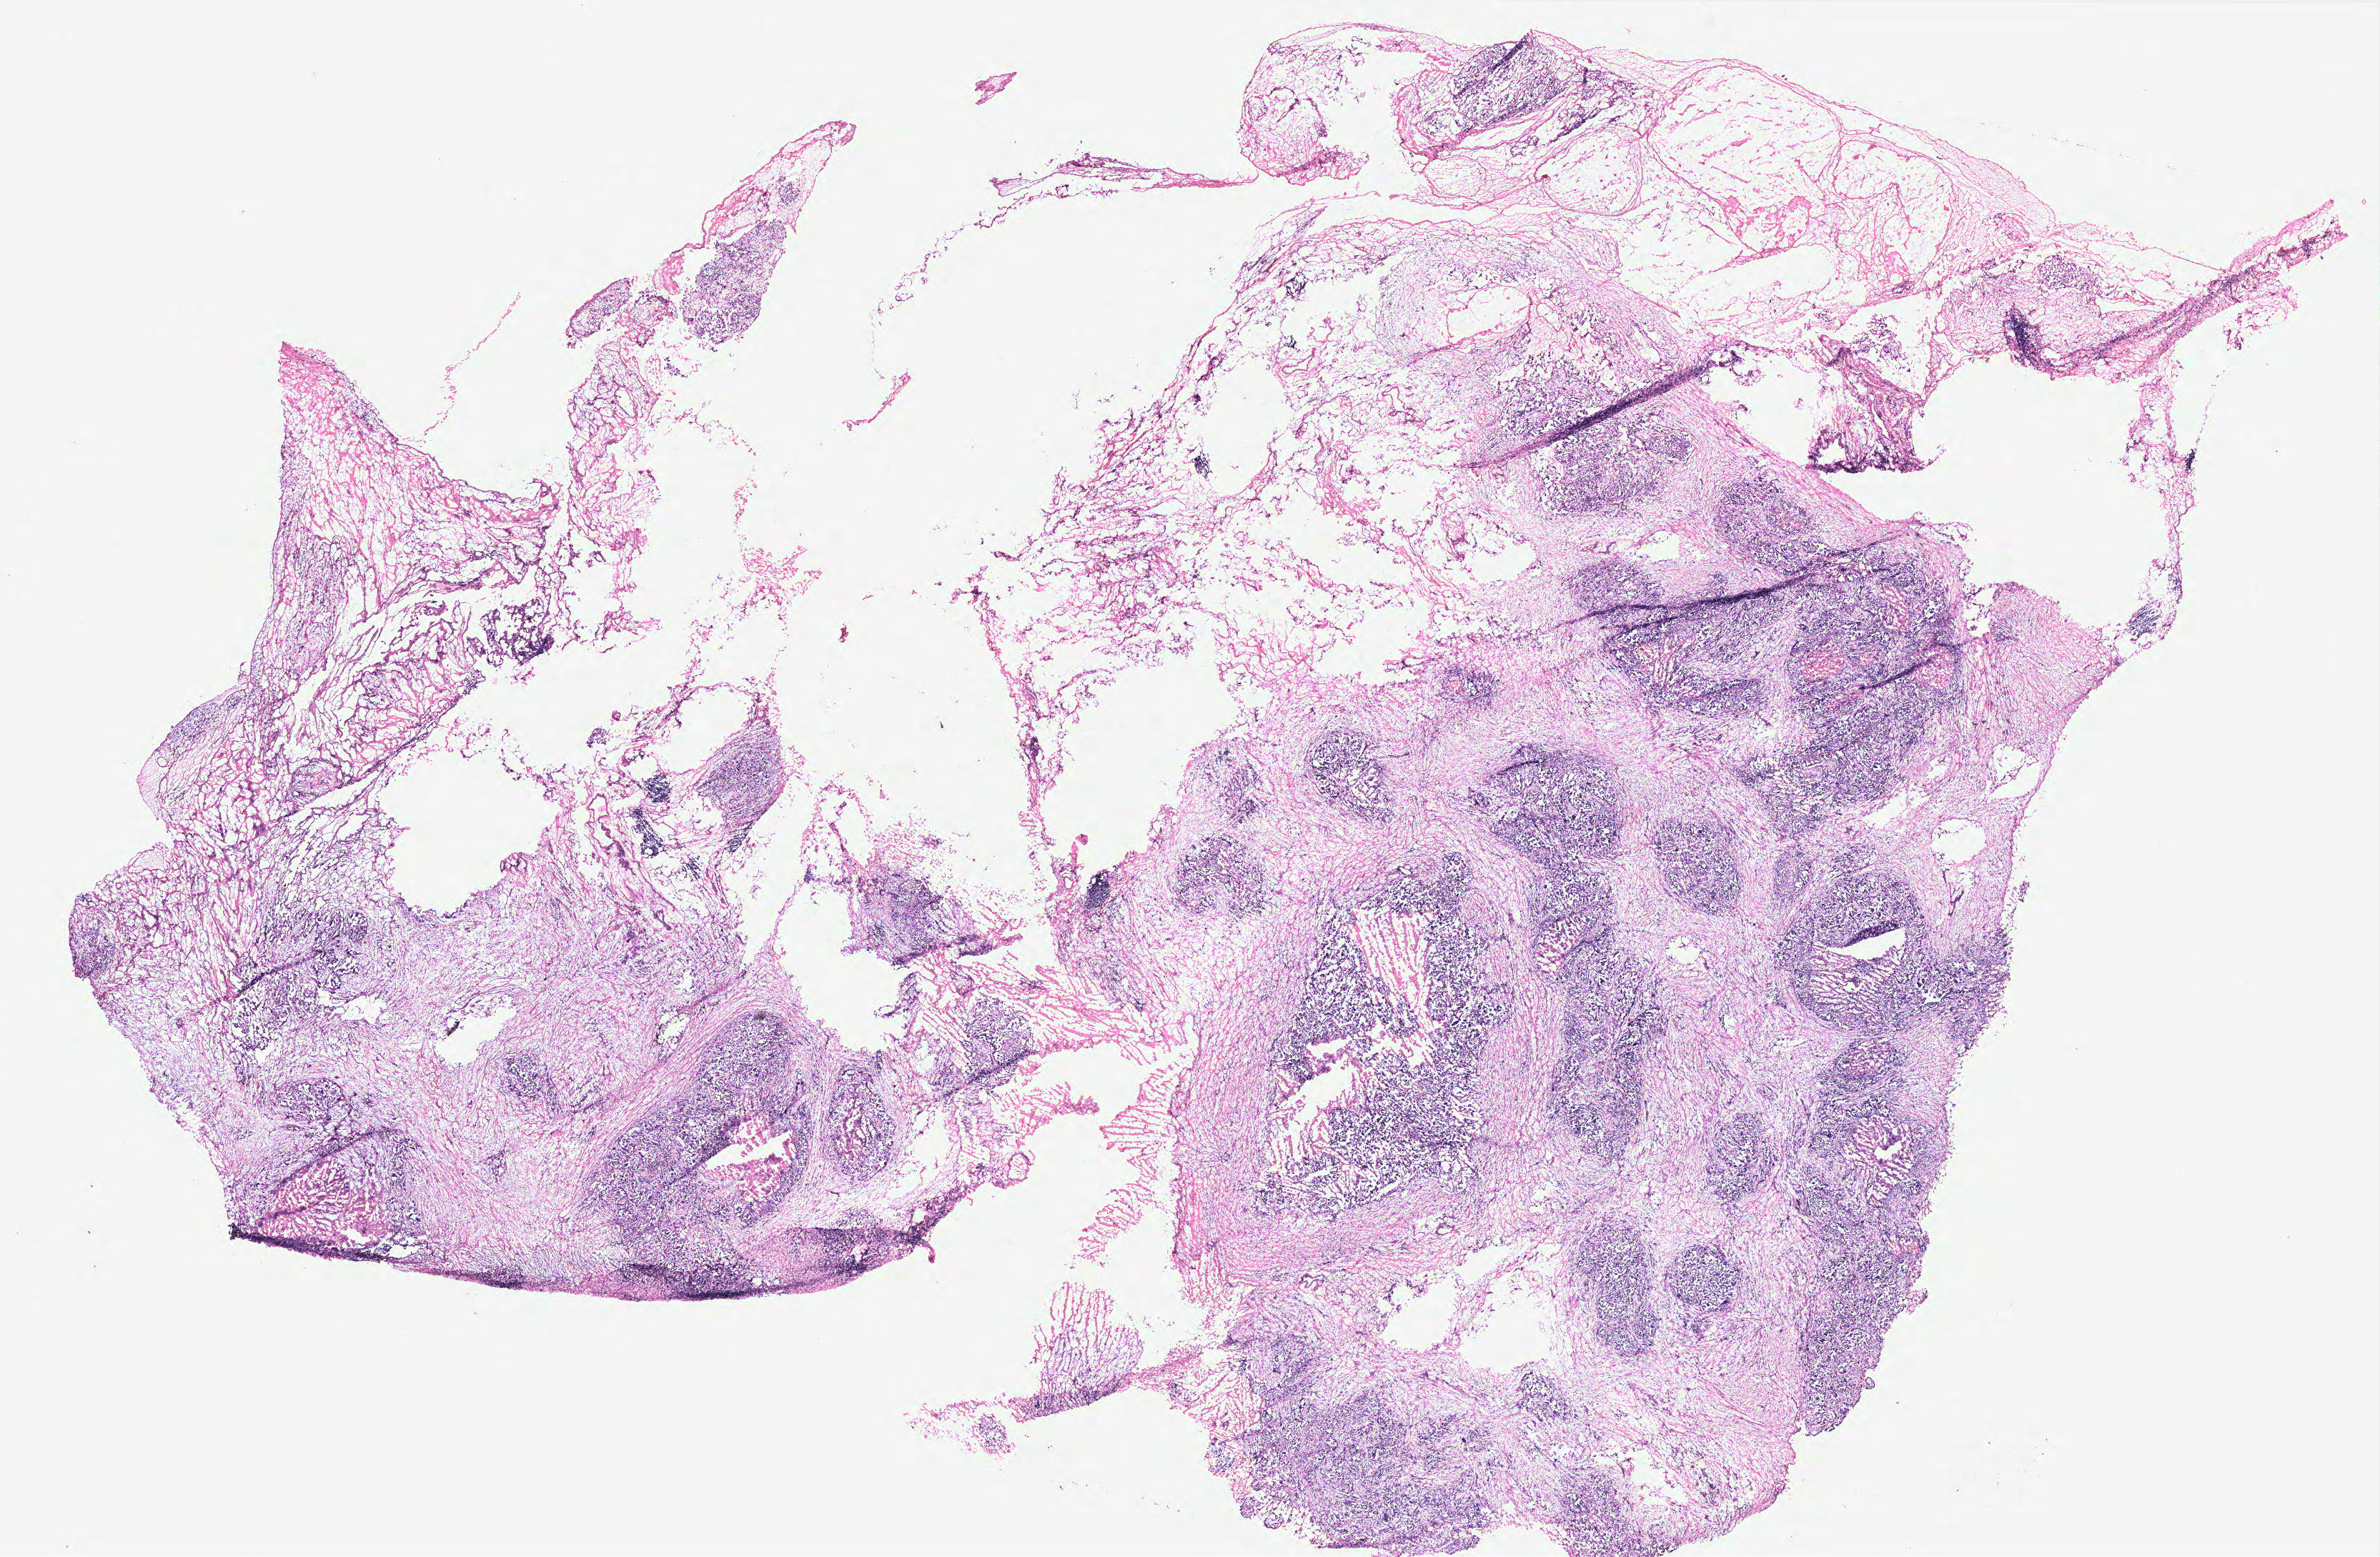
Whole-slide histology image, H&E — whole scanned area (about 26.7 x 17.4 mm, slide scanned at 40x) shown as a low-resolution overview; ovary, tumour tissue. 66-year-old female patient.
- primary tumour site (as recorded): ovary
- diagnosis: Serous adenocarcinoma, NOS